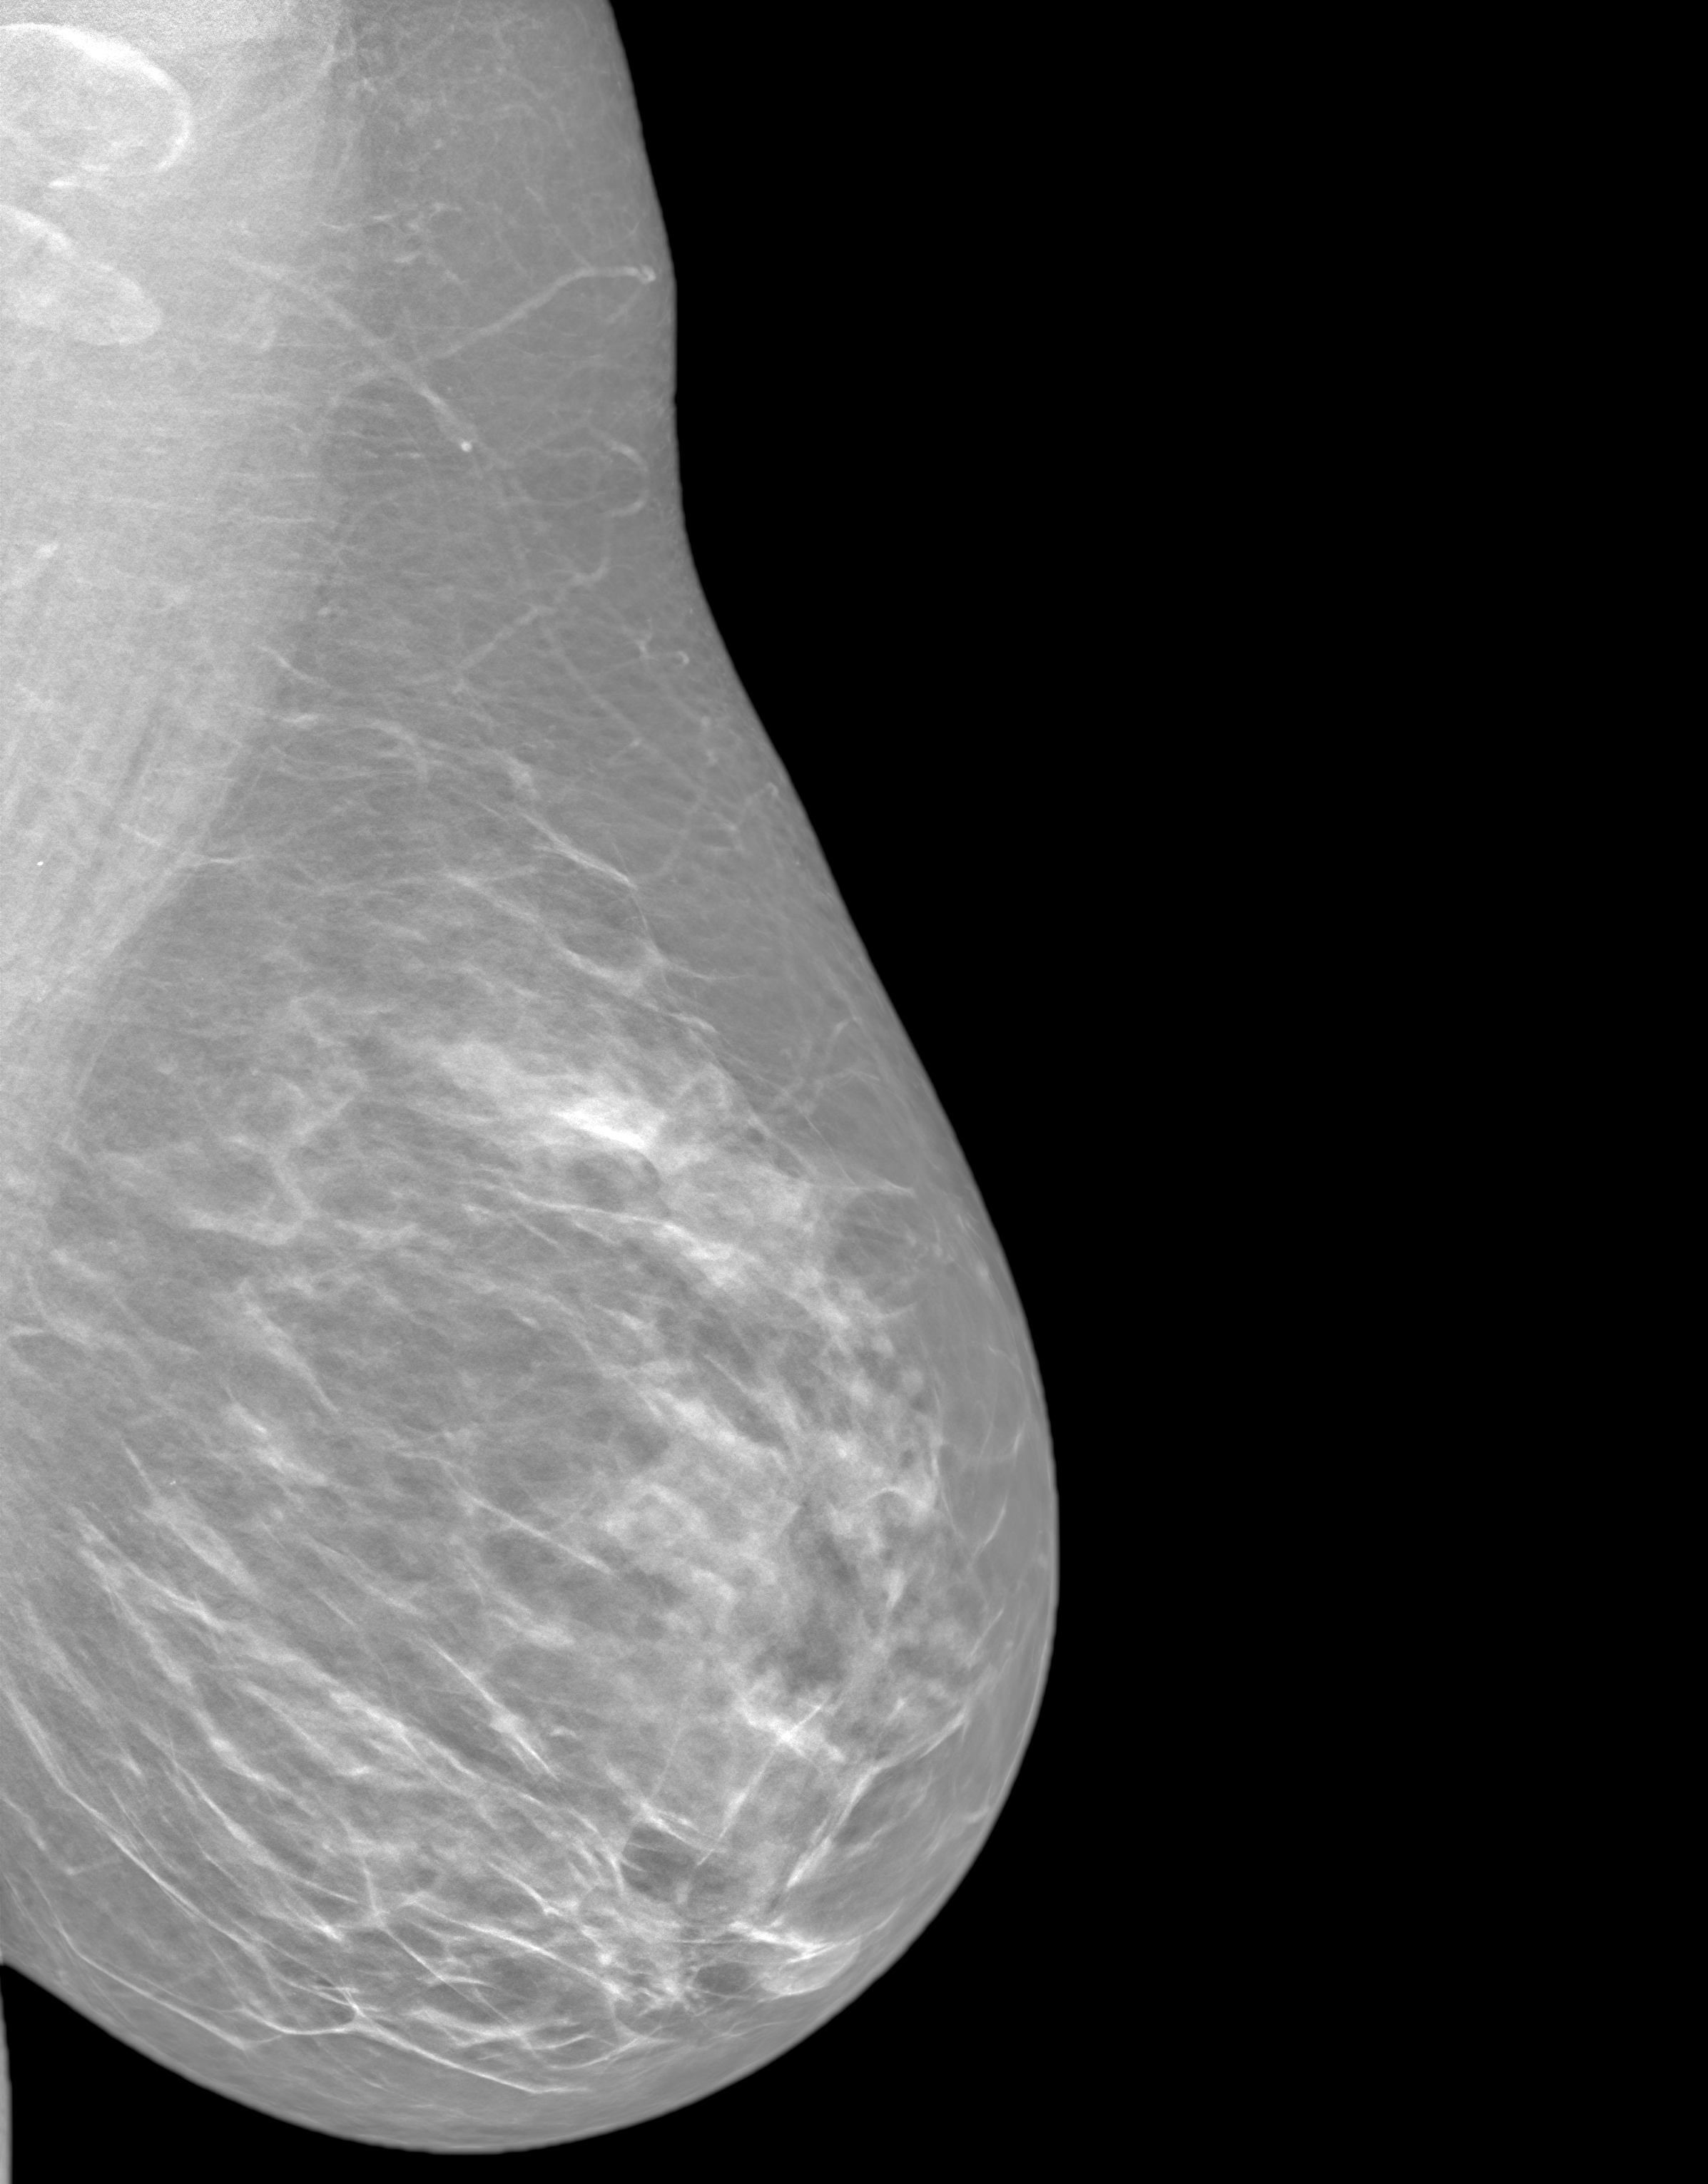
Synthesized 2-D mammogram reconstructed from digital breast tomosynthesis, left breast, medio-lateral oblique projection, annual screening mammography examination. Female patient, age 42 years.
Breast density at the screening exam (both breasts): heterogeneously dense (BI-RADS density category c). Final BI-RADS category for the screening round (tomosynthesis exam, both breasts): category 1. Recall: no recall after this screen.